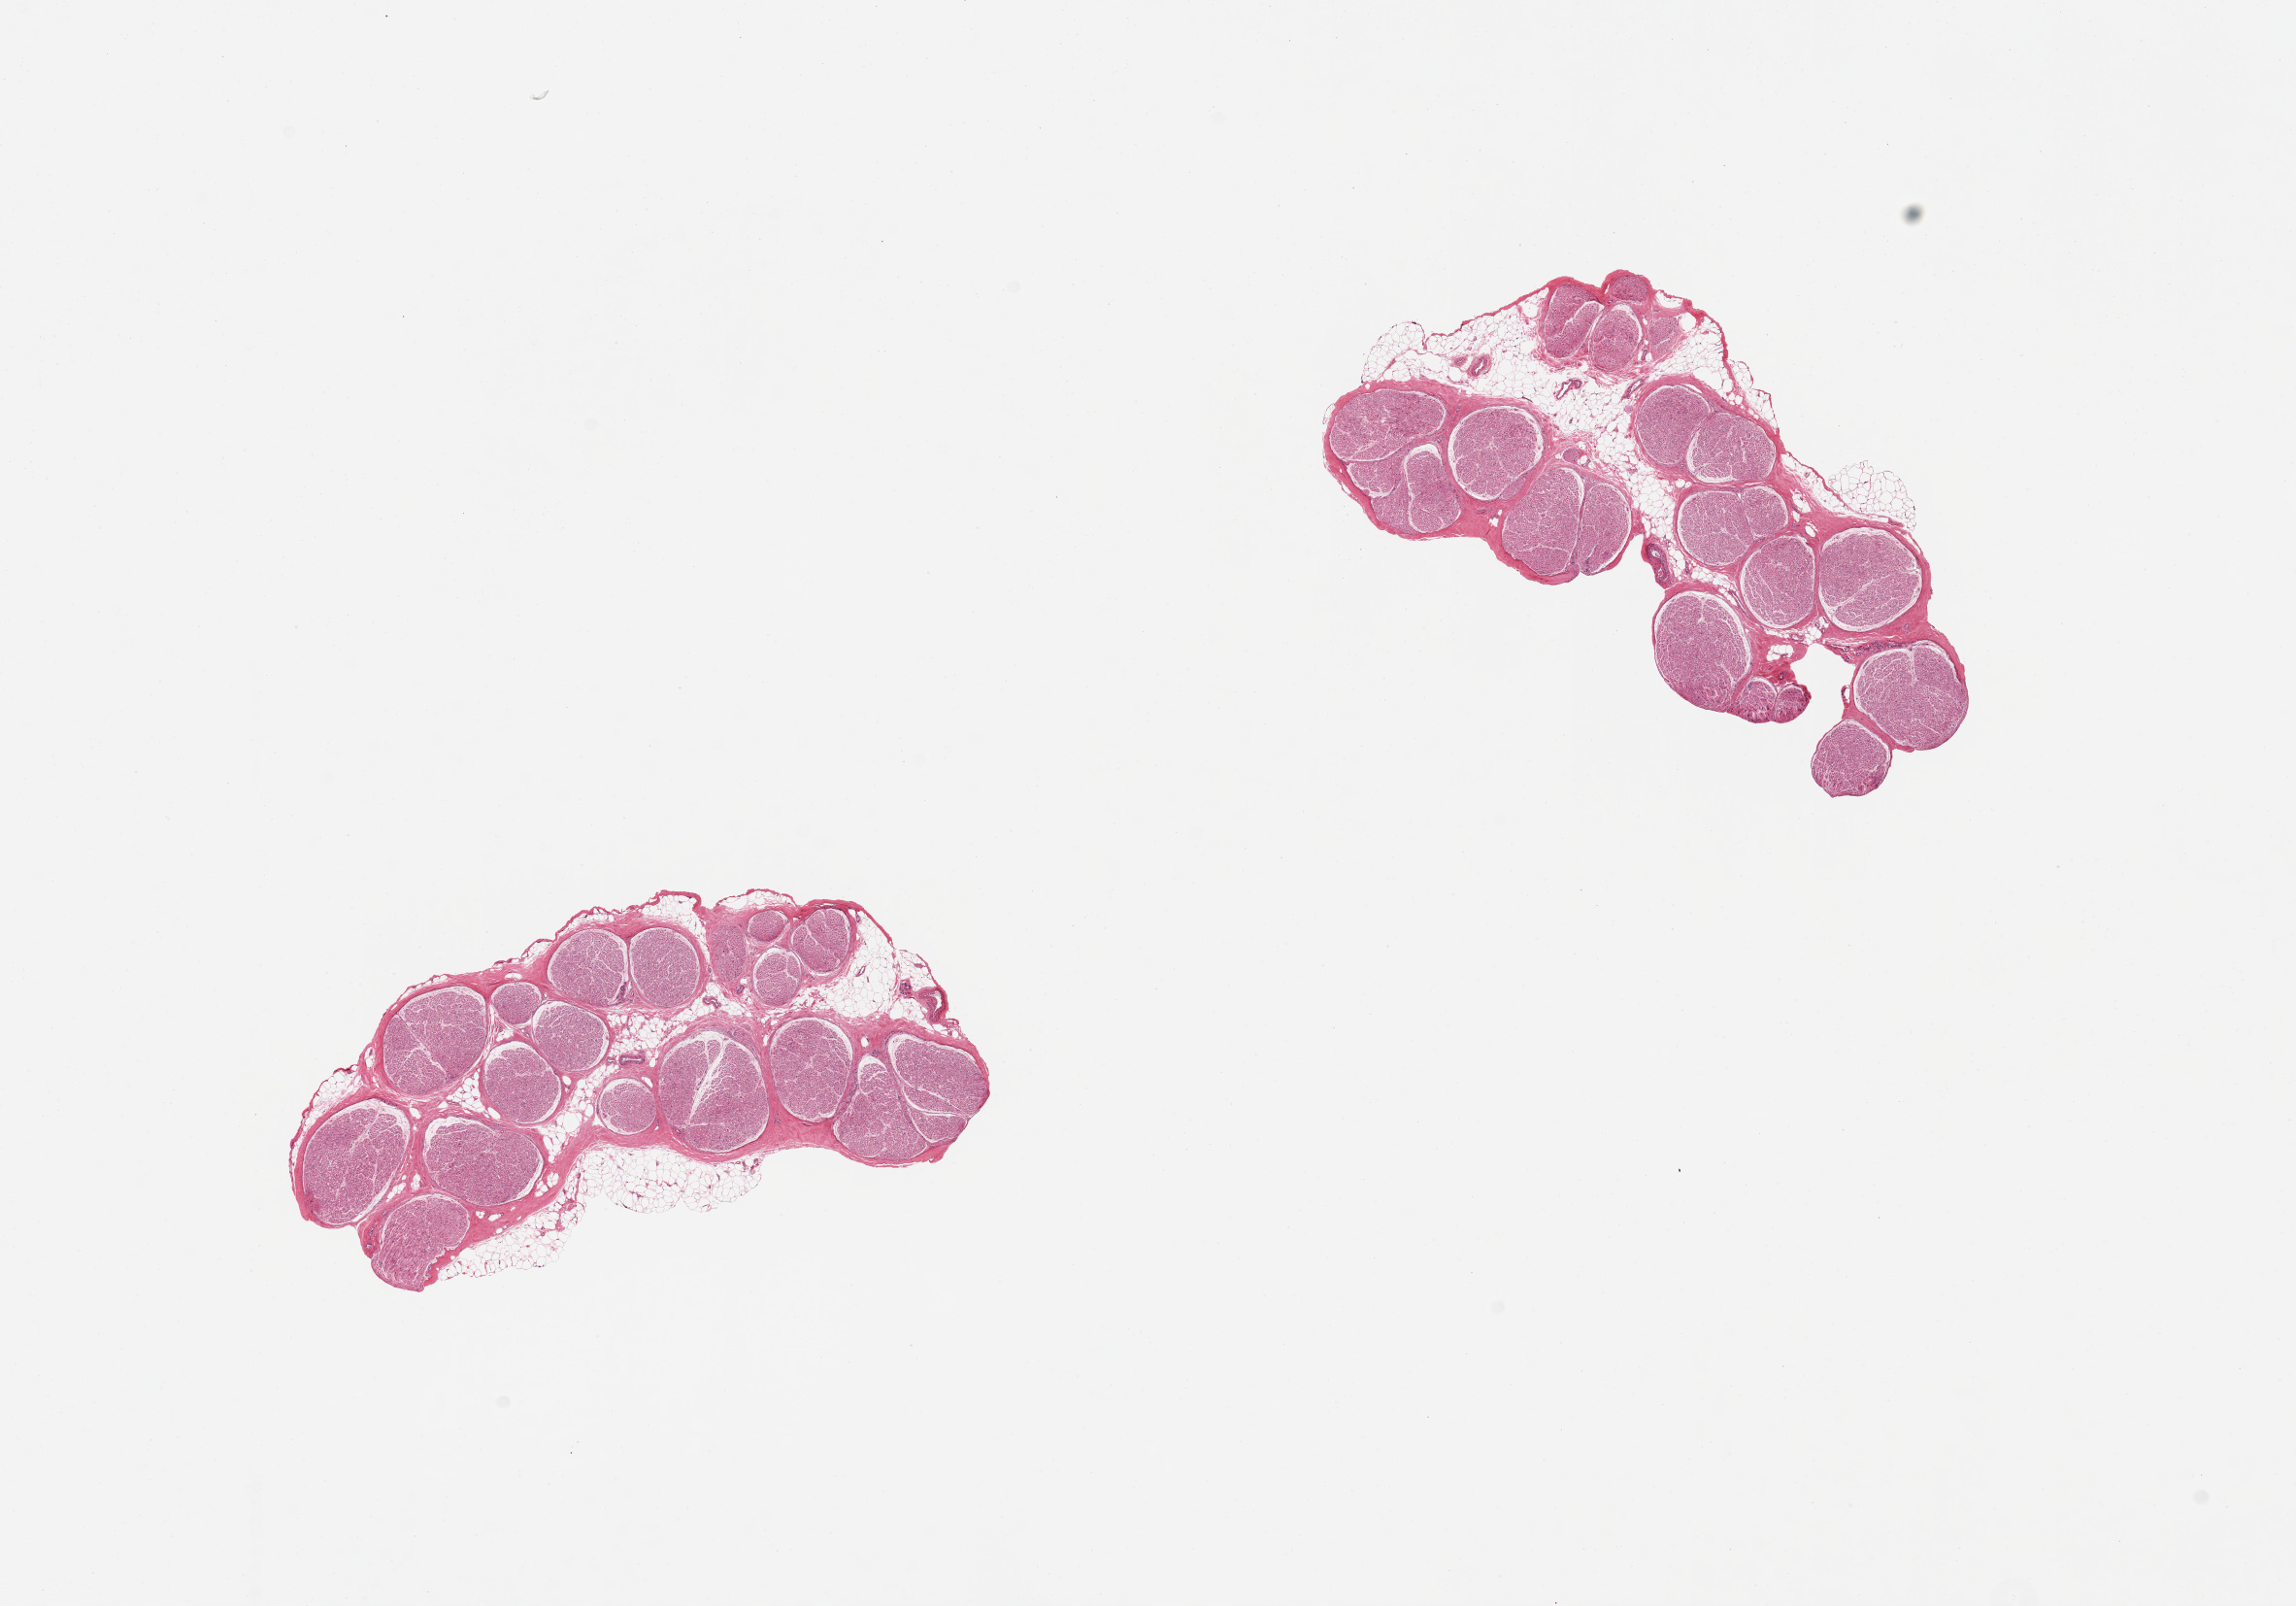
H&E whole-slide image — shown as a low-resolution overview of the whole scanned area (about 18.7 x 13.1 mm), PAXgene-fixed, paraffin-embedded tissue, target tissue: tibial nerve, tissue donor sample. Donor sex: female.
• review note (as recorded): 2 pieces, minimal adherent fat, good specimens